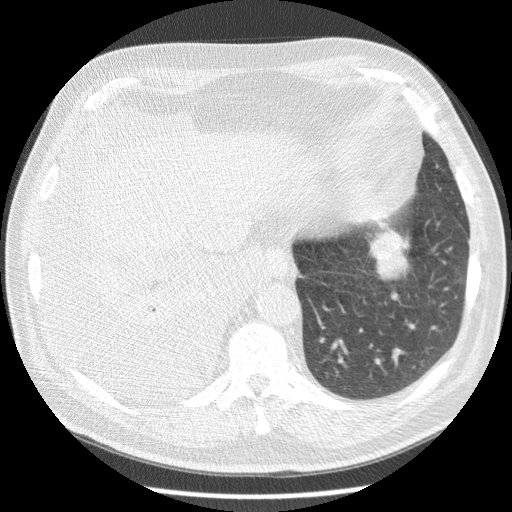
Low-dose screening chest CT, one axial slice. Position 52 of 180 along the scan axis. 120 kVp. Lung window (W 1500 / L -600 HU). 2.5 mm slice thickness. 512 × 512 image matrix, field of view 355 × 355 mm.
Annotated regions visible in this slice (manually delineated by an expert):
- lesion 1 (tumor, lower lobe of left lung): bounding box <370,230,408,279> (left, top, right, bottom; pixels)